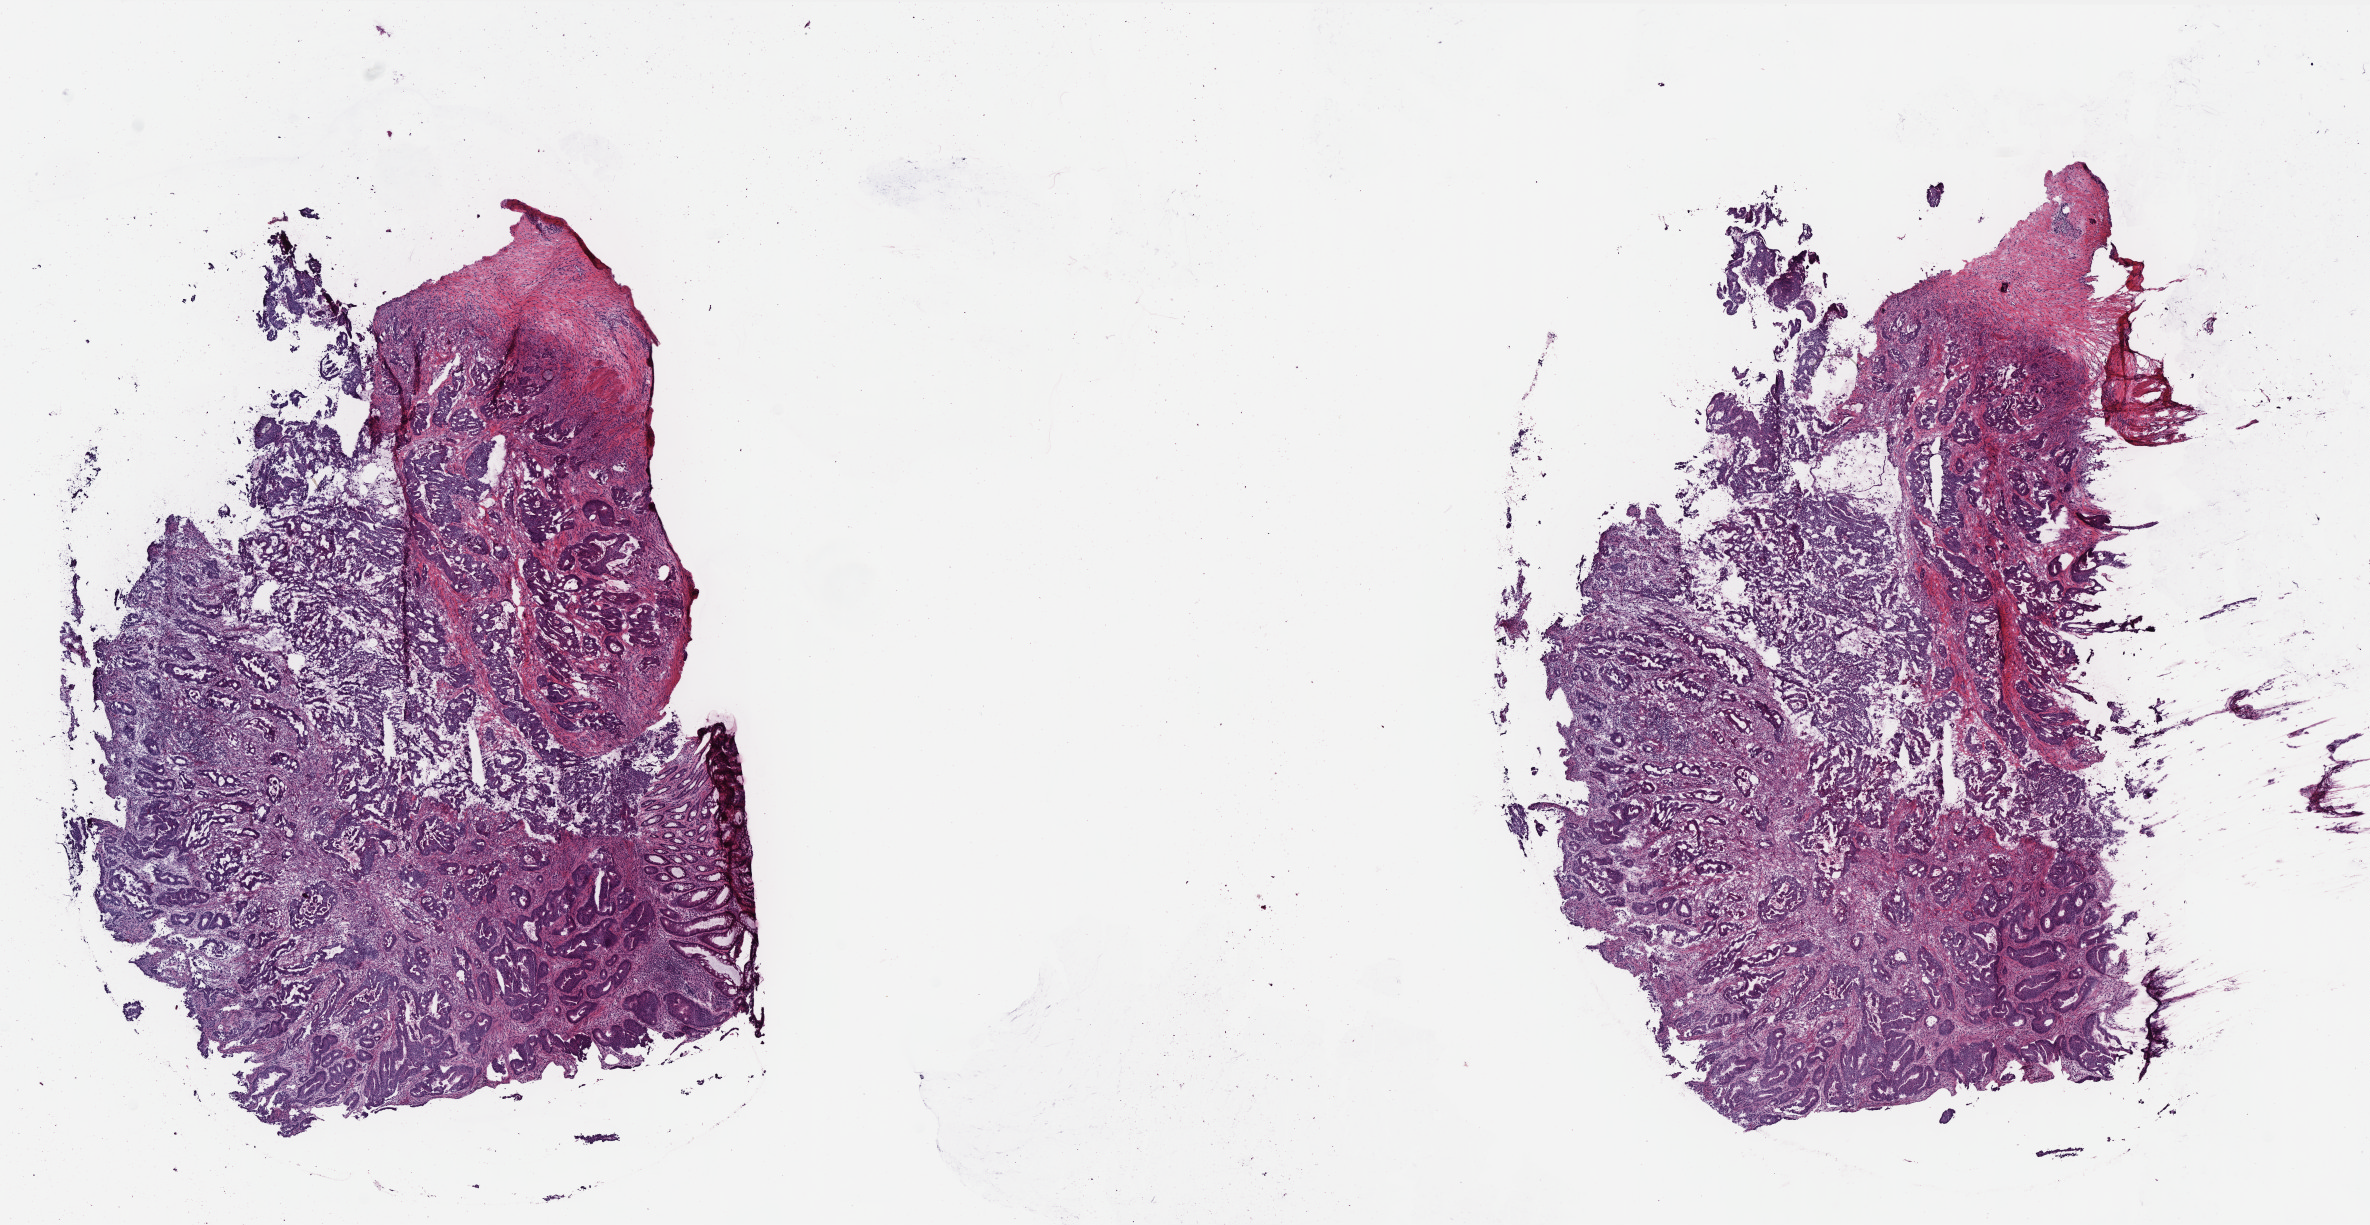
Whole-slide histology image, H&E-stained, shown as a low-resolution overview of the whole scanned area (about 19.0 x 9.8 mm, acquisition: 40x scan); frozen section from the bottom of the tissue portion; primary tumour sample from the rectum. Patient: male, age at initial diagnosis 55 years. Pathologist review of this section (percent, as recorded): tumour cells 81%, tumour nuclei 65%.
Histologic diagnosis: Adenocarcinoma, NOS.